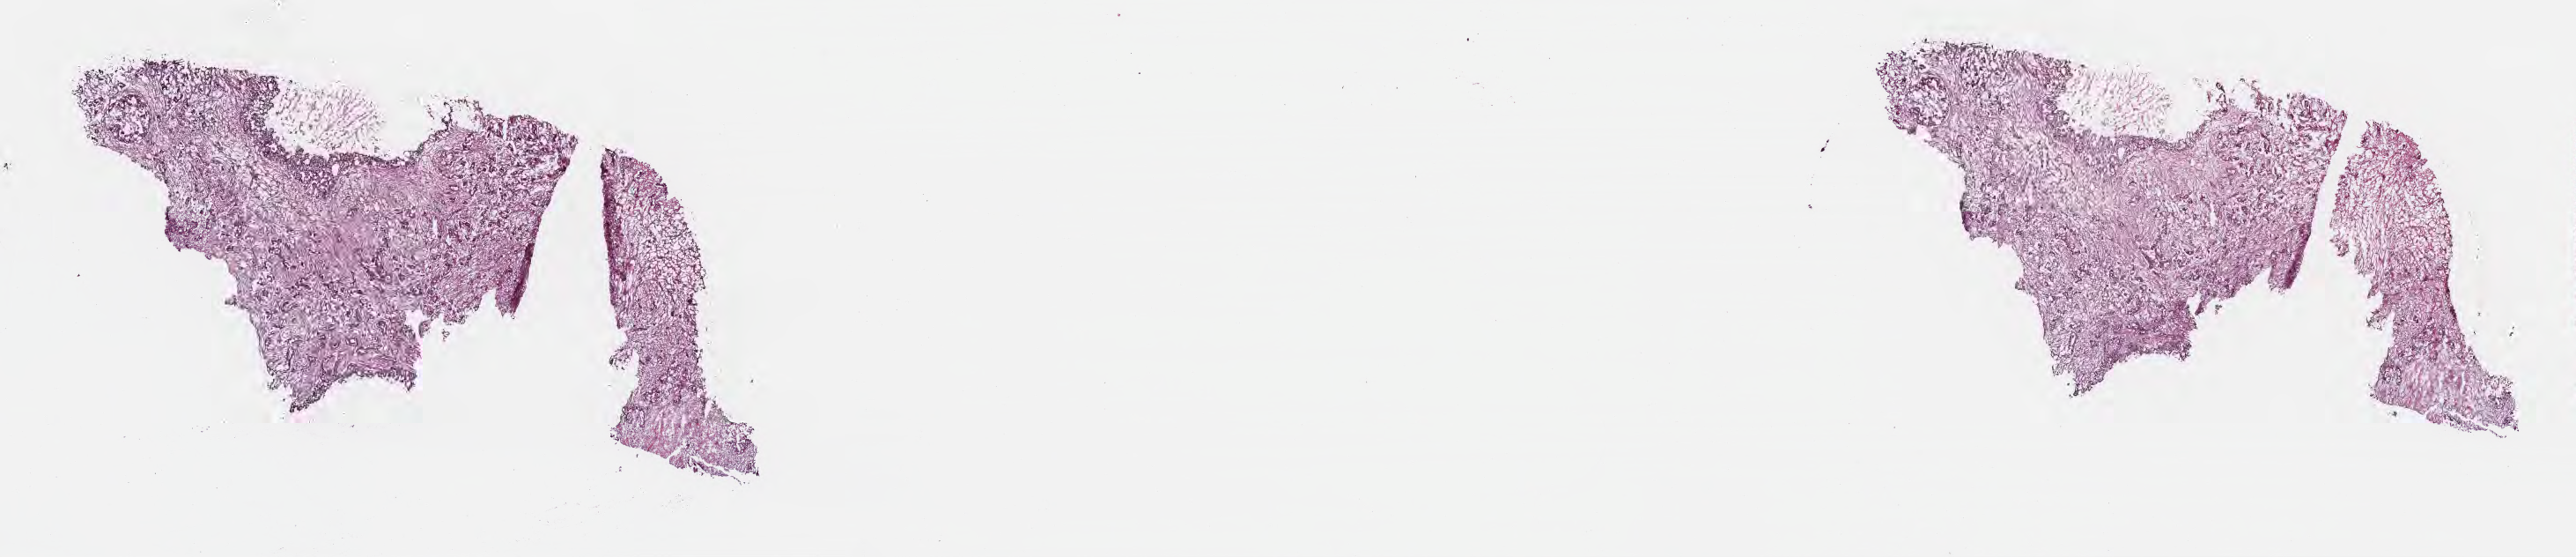
Hematoxylin and eosin (H&E) whole-slide image — whole scanned area (about 23.7 x 5.1 mm) shown as a low-resolution overview. Frozen section (tissue freezing medium). Primary tumor. Anatomic site: head of pancreas. Male patient; age at initial diagnosis 74 years.
Diagnosis: Intraductal papillary mucinous neoplasm with invasive carcinoma.